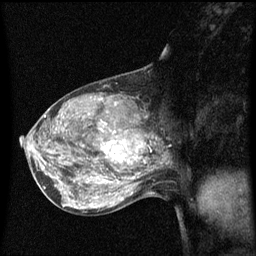
Breast MRI (dynamic contrast-enhanced), one sagittal slice; position 31 of 60 along the scan axis; dynamic contrast-enhanced series, image 2 of 3 at this slice position (ordered by acquisition); 1.5 T; TE 4.2 ms, TR 8.4 ms; 2 mm slice thickness; 256 × 256 image matrix. Female patient, age 50 years.
Annotated regions visible in this slice (semi-automatically segmented with operator editing):
- analysis volume of interest (the breast-tissue region the enhancement analysis was run in; not a lesion): box from (x=100, y=114) to (x=153, y=171) px
- tumour enhancement mask (voxels above the 70 % enhancement threshold inside the analysis volume of interest): (x=100, y=124)–(x=145, y=163)